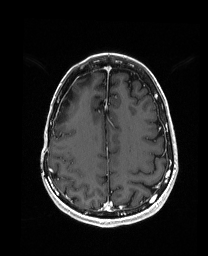
Brain MRI from a brain-tumour surgery series, one axial slice; slice 57 of 192 in the series (ordered by position); T1-weighted post-contrast; 1 mm slice thickness; 208 × 256 image matrix. From the clinical record (not read from this slice): histopathology: Metastatic Carcinoma from Breast primary; tumour location: Right Frontal.
Annotated regions visible in this slice (expert manual segmentation):
- previous resection cavity: bounding box <62,88,73,106> (left, top, right, bottom; pixels)